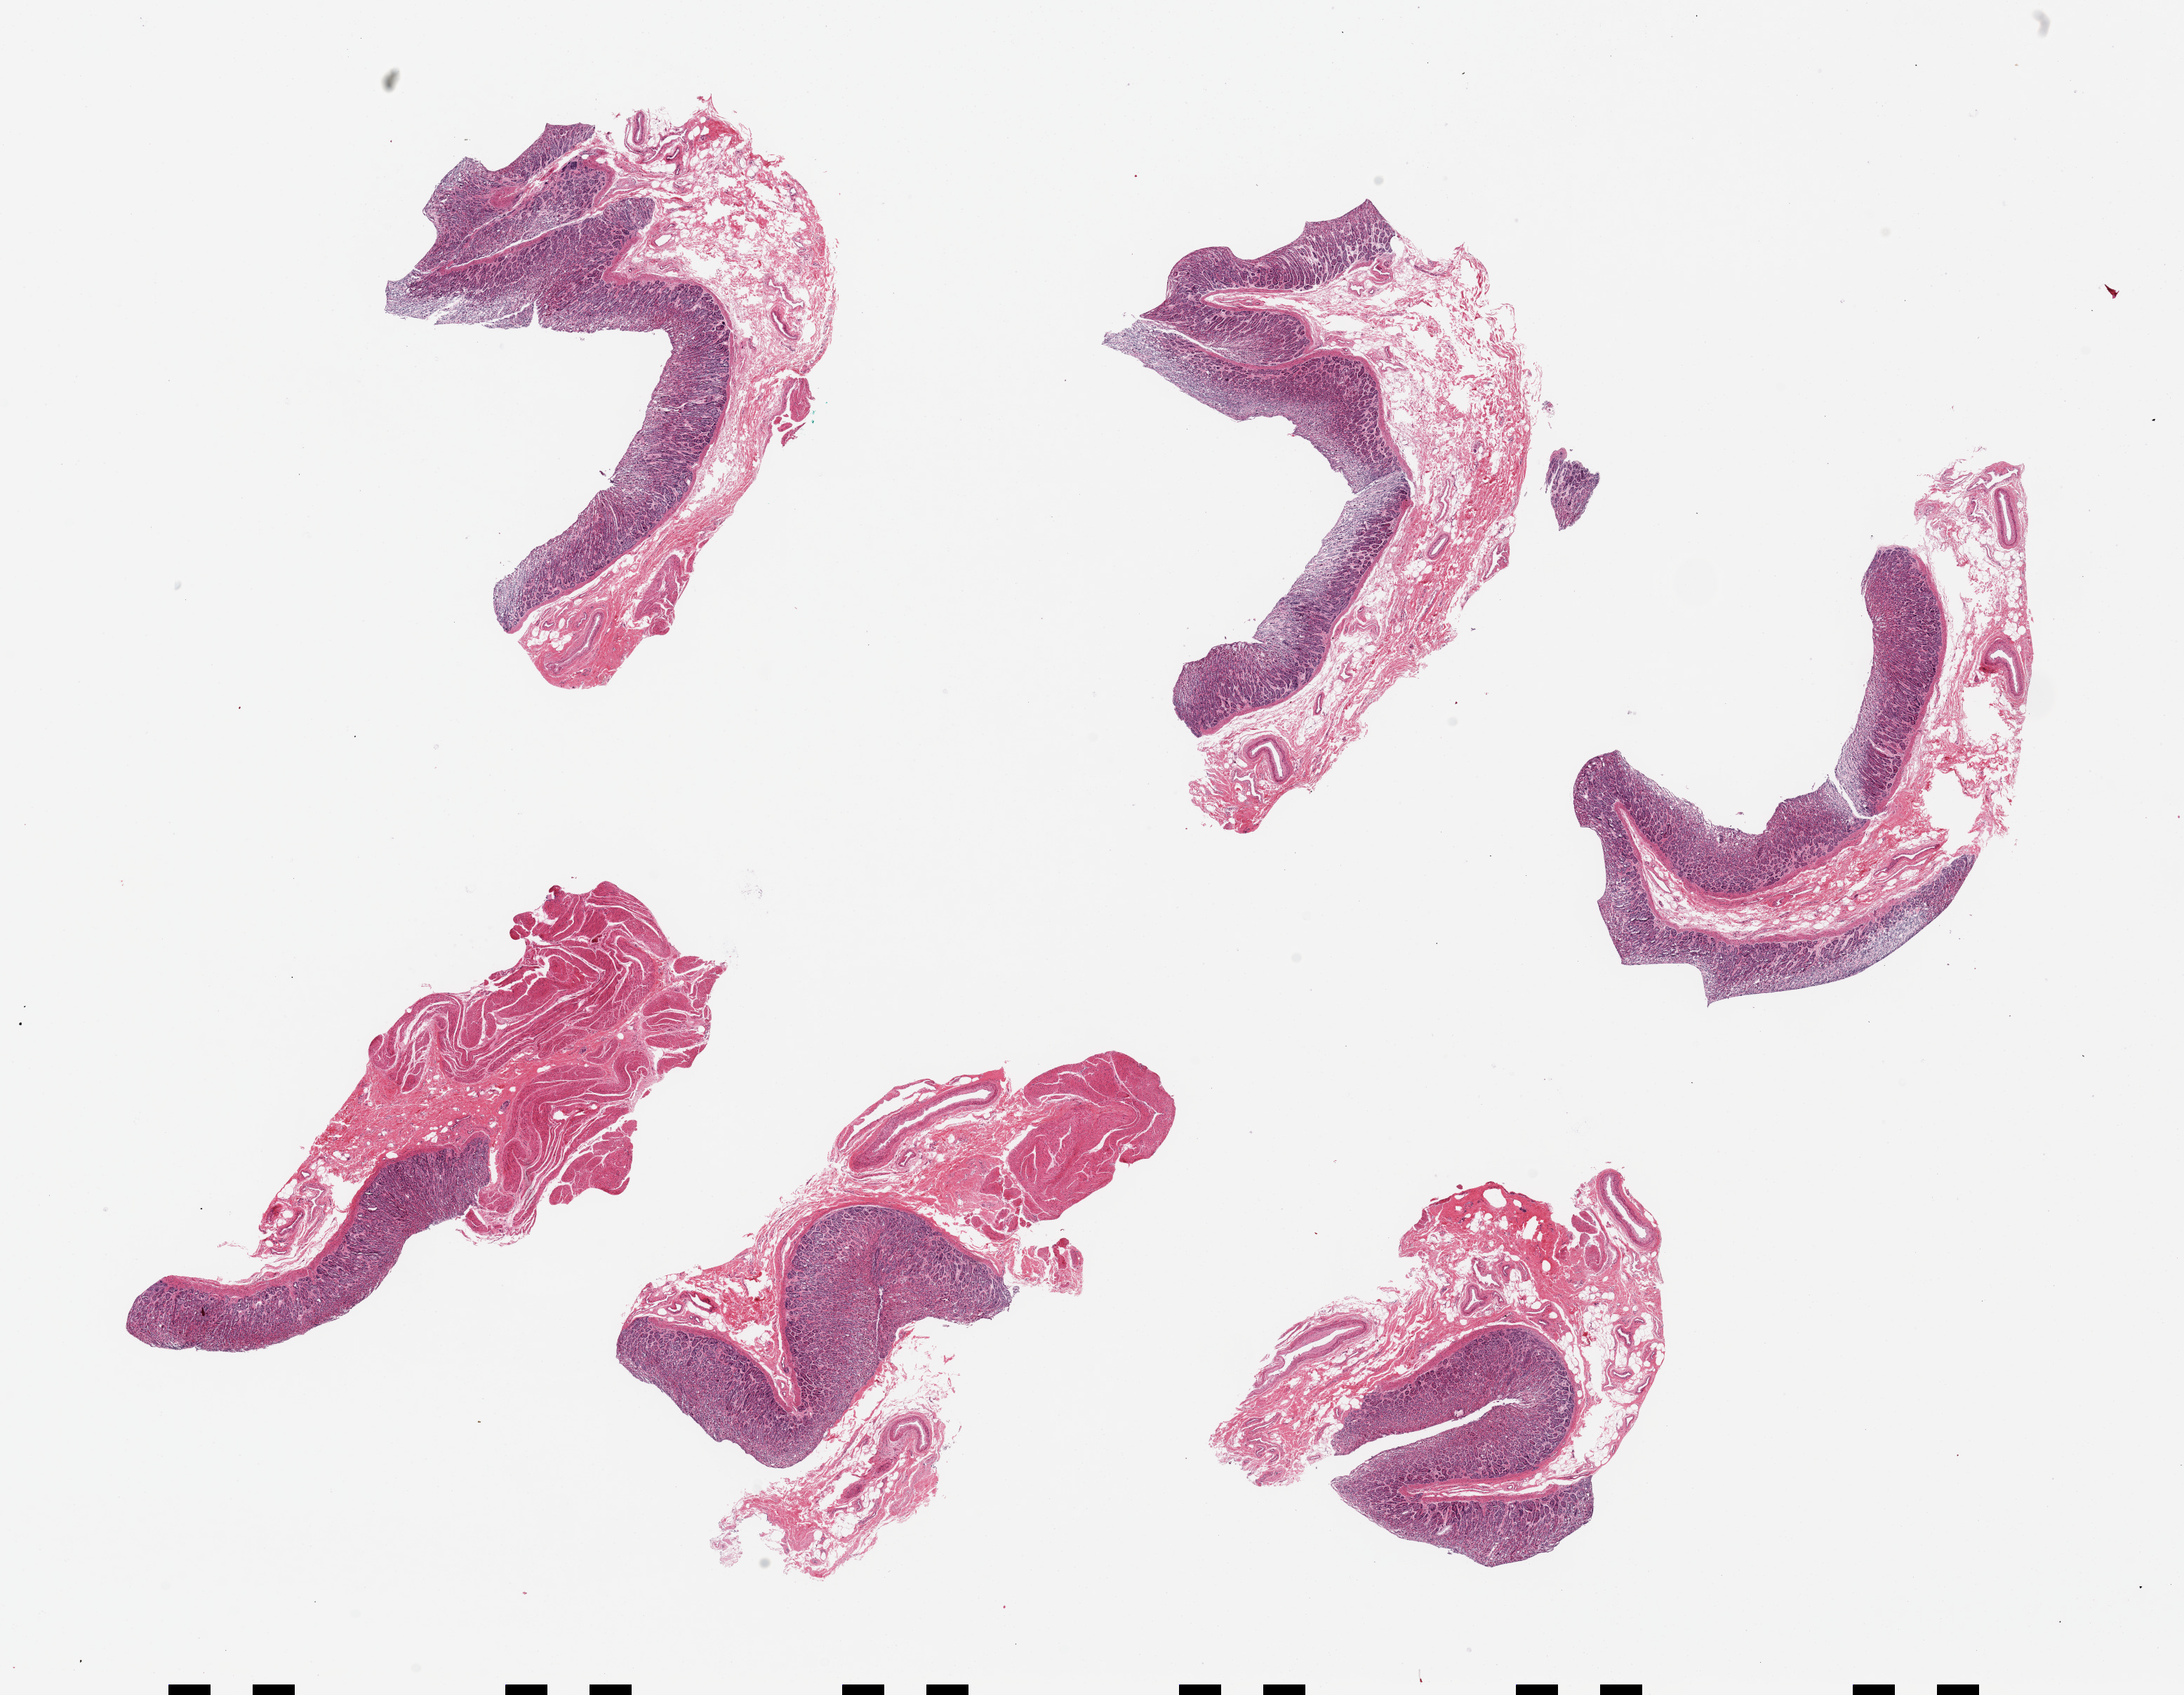
Digitized H&E-stained section, brightfield, a low-resolution overview of the entire scanned area, about 24.6 x 19.1 mm; PAXgene-fixed paraffin-embedded (PFPE) section; target tissue: stomach; tissue donor sample.
Pathologist's review note for this sample: 6 pieces `~7x2mm. Mucosa variably preserved (1-2), ~30-40% of thickness.